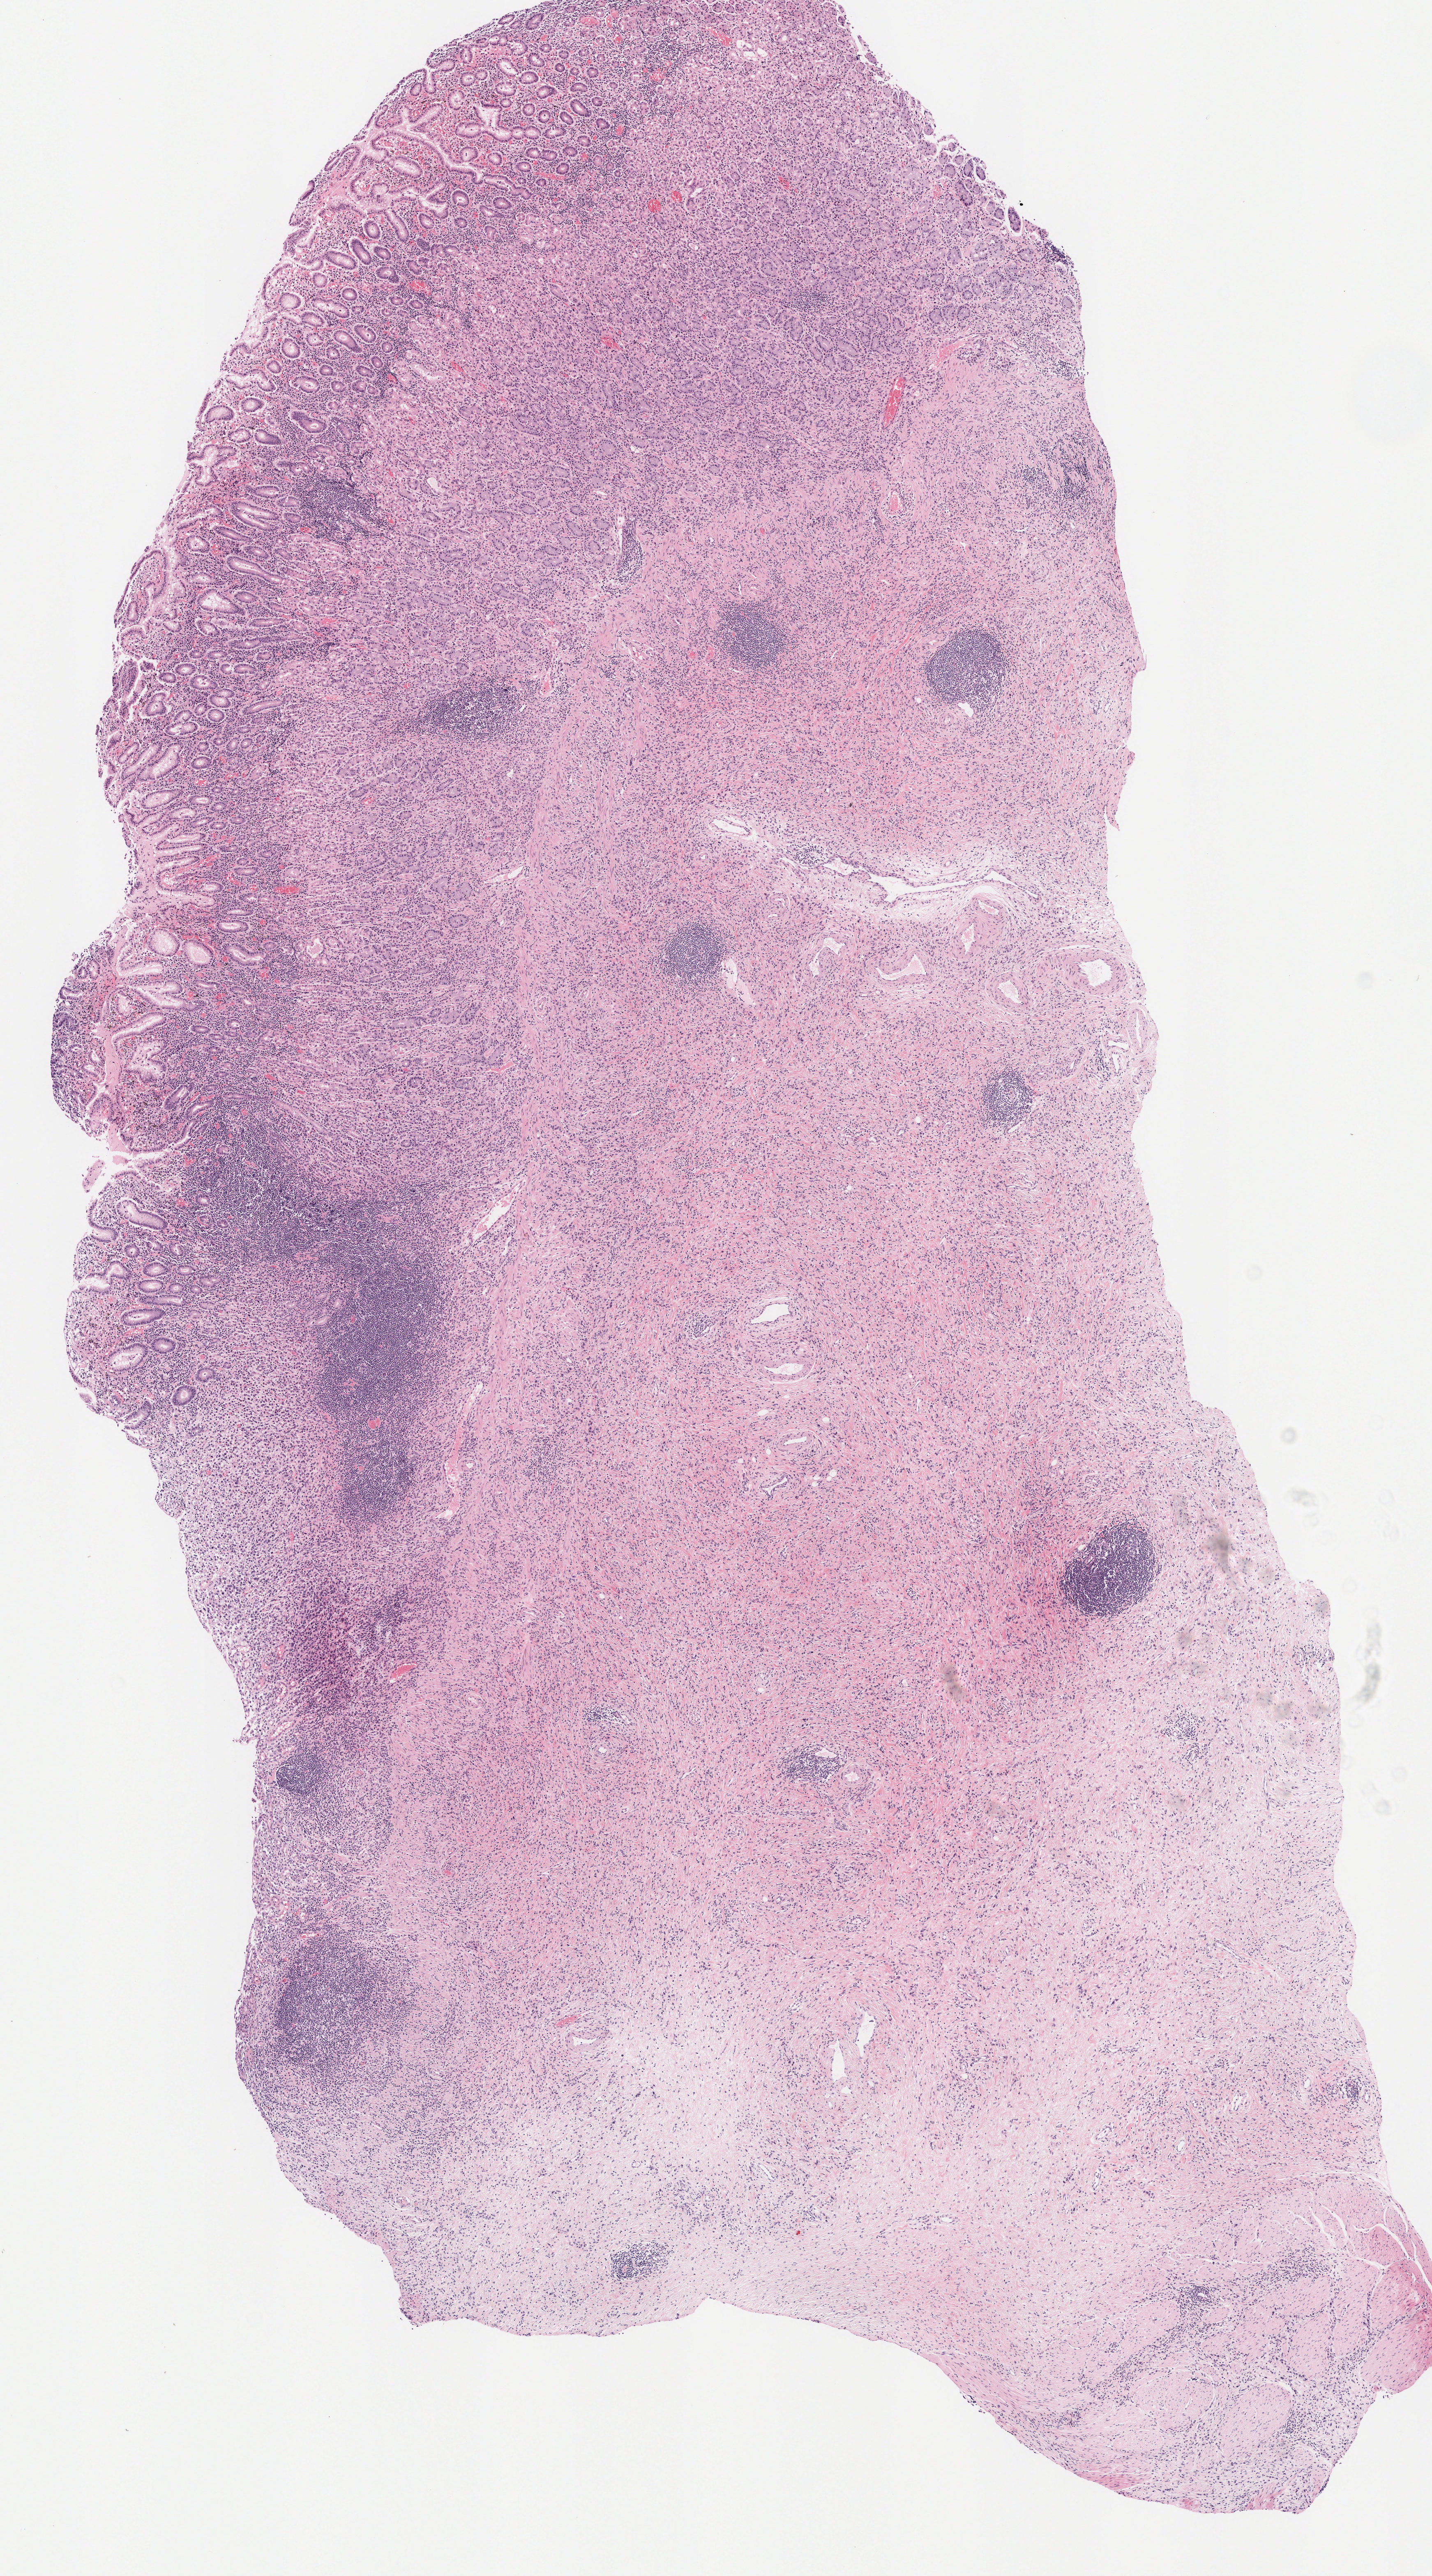
Digitized Hematoxylin and eosin (H&E) stained tissue section (whole slide) — a low-resolution overview of the entire scanned area, about 6.9 x 12.4 mm (from a 20x scan), formalin-fixed paraffin-embedded (FFPE) diagnostic section, primary tumour sample from the stomach. Female, age 60 years at initial diagnosis.
Histologic diagnosis: Carcinoma, diffuse type (gastric antrum).